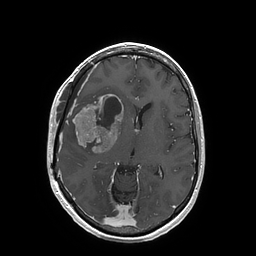
Brain MRI from a brain-tumour surgery series, one axial slice. Slice 89 of 202 in the series (ordered by position). T1-weighted post-contrast. 1 mm slice thickness. 256 × 256 image matrix, field of view 250 × 250 mm. Case-level facts recorded for this patient, not image findings: histopathology: Glioblastoma; WHO grade: 4; IDH mutation: no.
Outlined on this slice (outlined manually by an expert reader):
- tumour: bounding box [x1, y1, x2, y2] px = [73, 94, 123, 153]